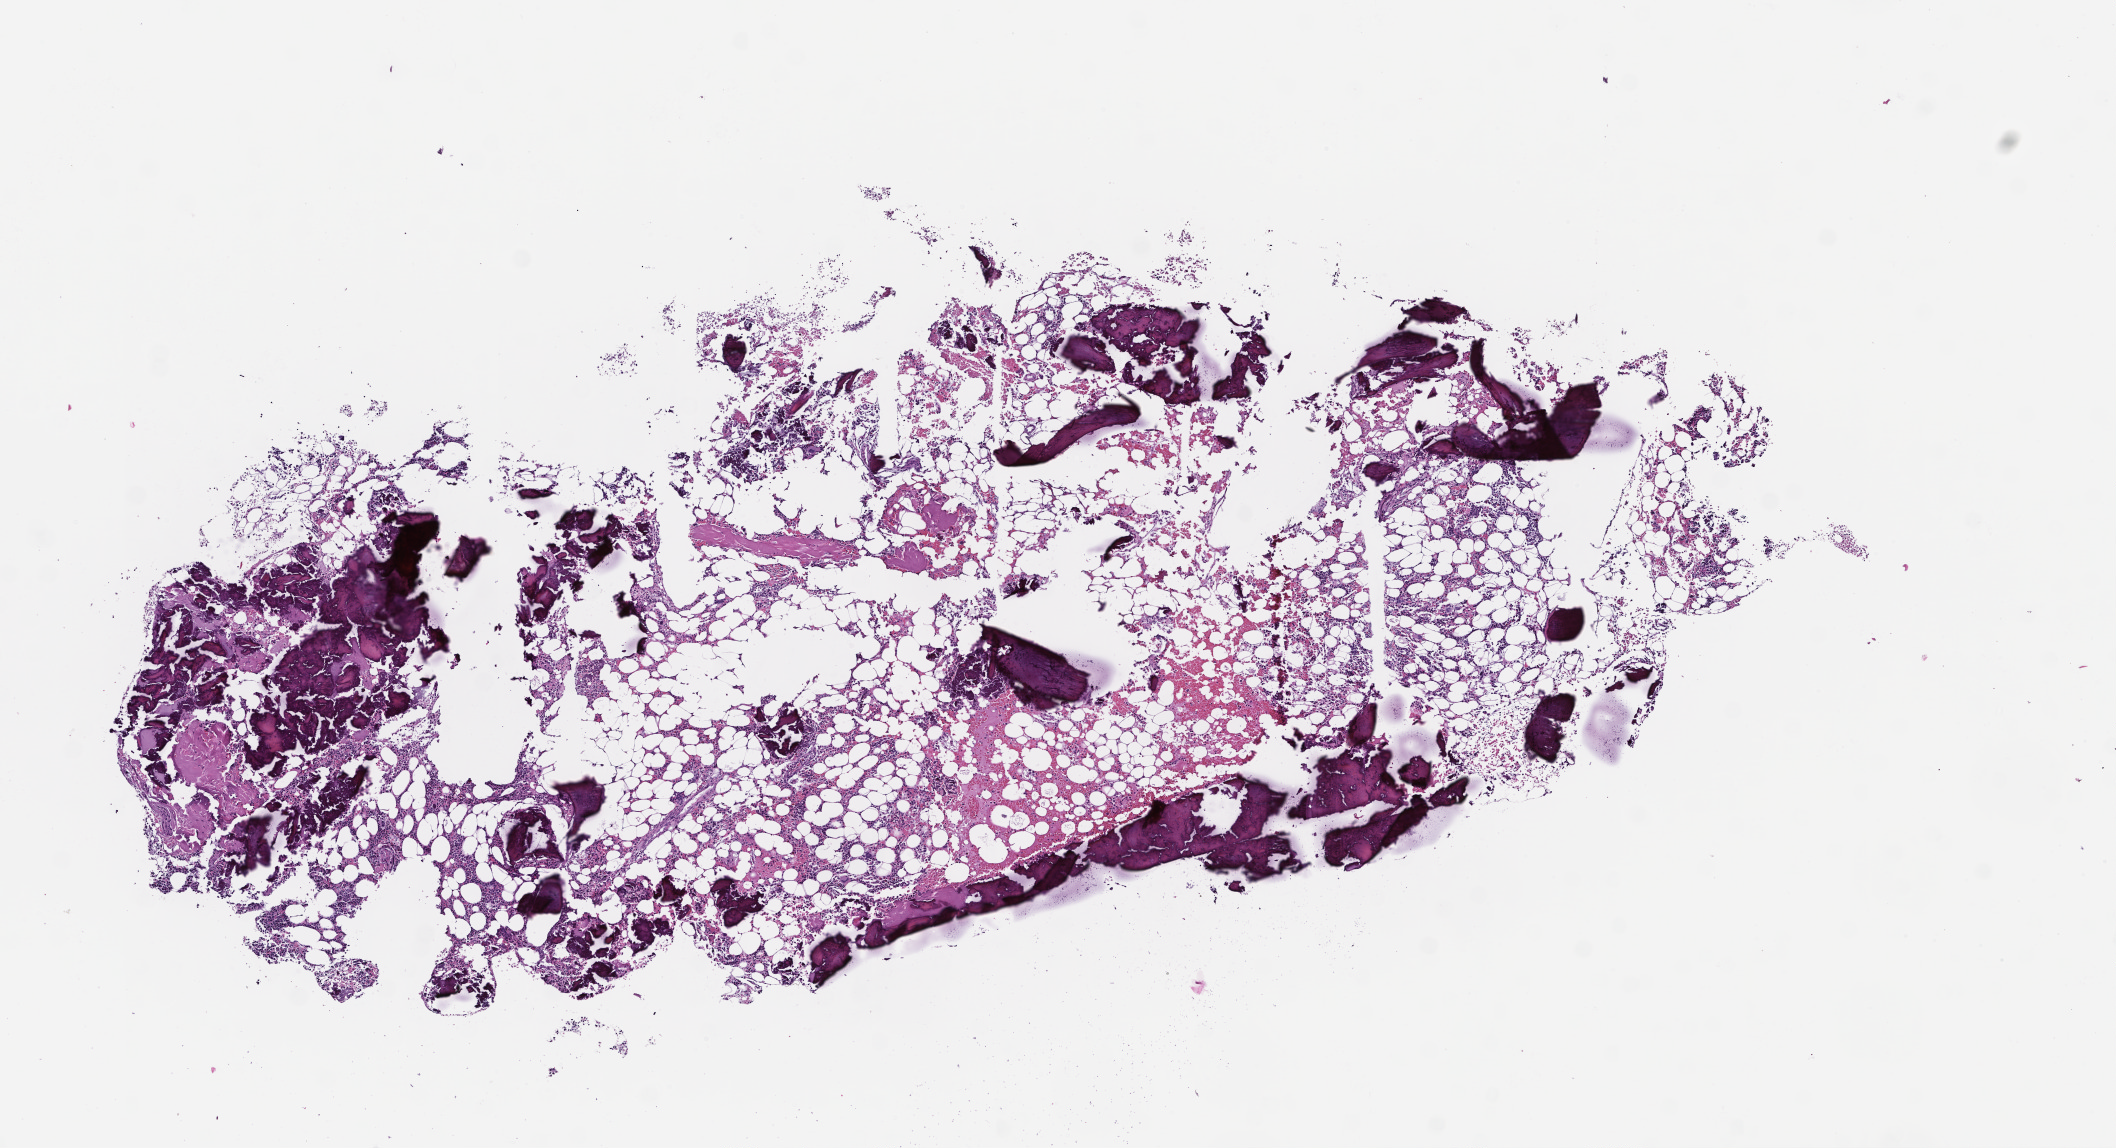
Haematoxylin and eosin whole-slide image, whole scanned area (about 8.5 x 4.6 mm) shown as a low-resolution overview; formalin-fixed paraffin-embedded section; site: bone marrow; collected on treatment. Patient: male.
- this section: primary tumor
- diagnosis: Plasma Cell Myeloma